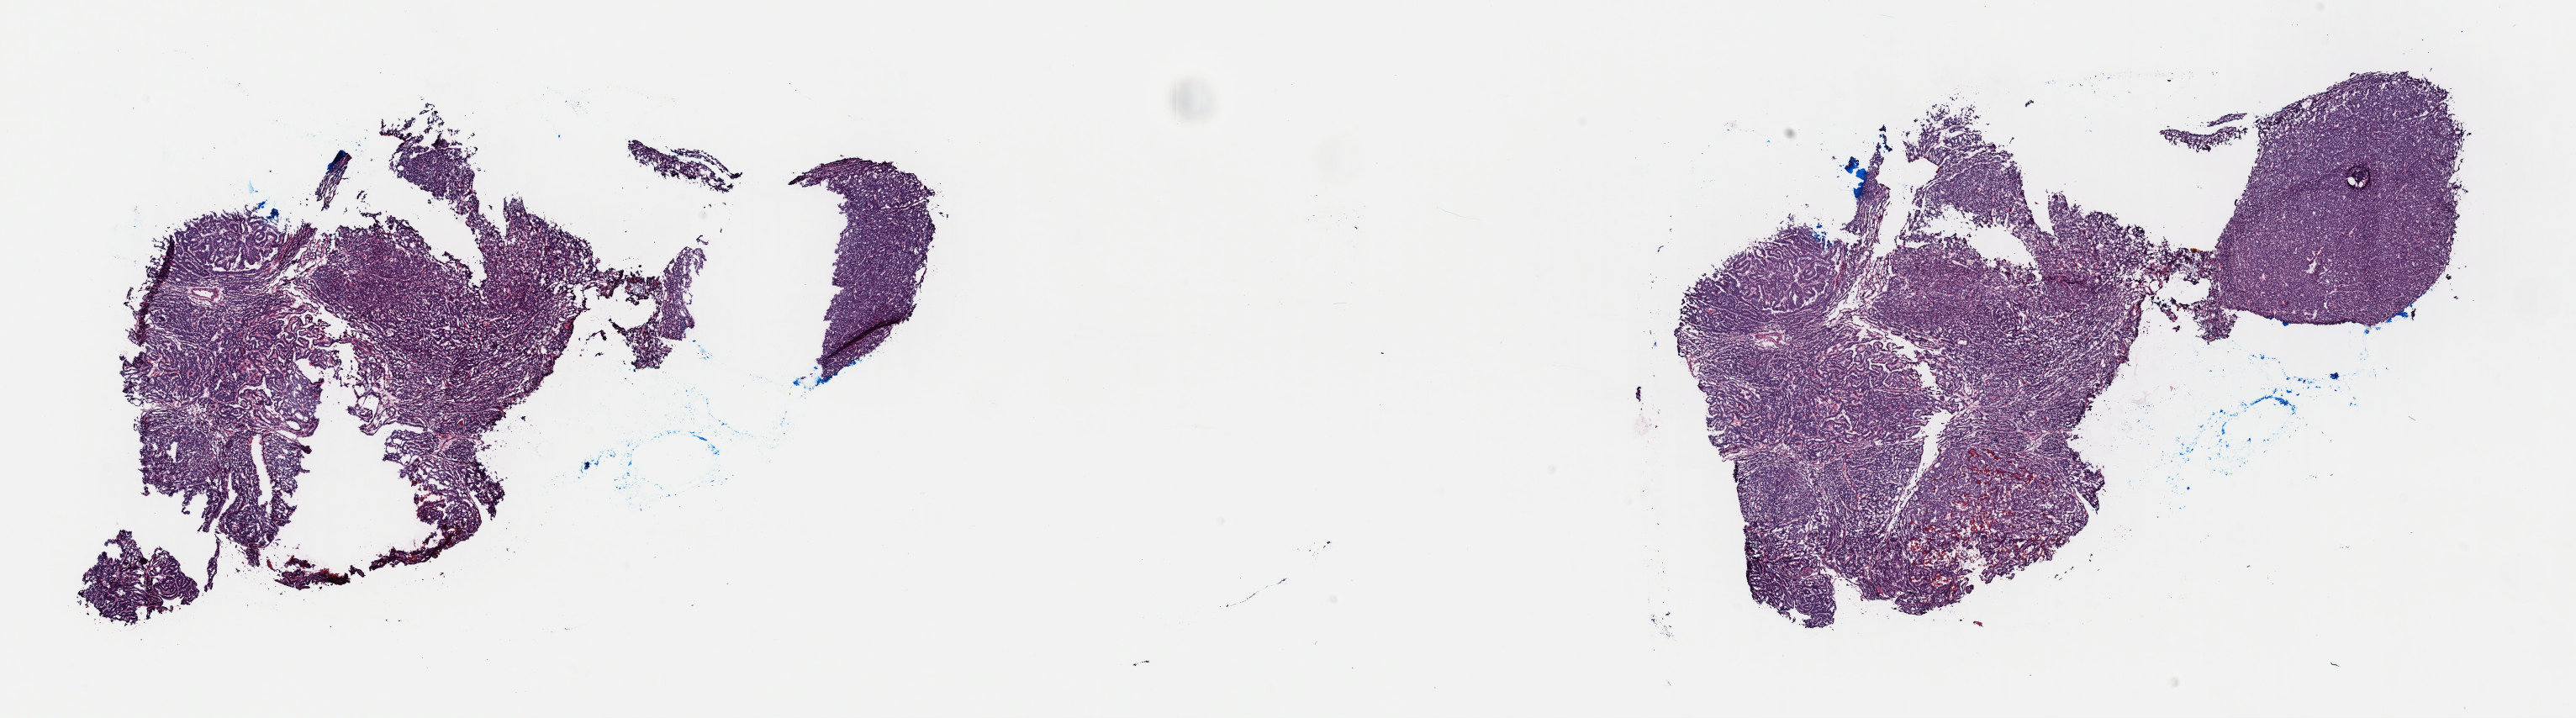
Digitized Hematoxylin and eosin (H&E) stained tissue section (whole slide), a low-resolution overview of the entire scanned area, about 24.2 x 6.7 mm (from a 40x scan), frozen section from the top of the tissue portion, sample: primary tumour, thyroid. Patient: female, age at initial diagnosis 51 years. Slide review estimates, as recorded: tumour cells 95%, tumour nuclei 95%, normal cells 0%, stromal cells 5%, necrosis 0%. Inflammatory infiltration, as recorded: lymphocyte infiltration 1%, monocyte infiltration 0%, neutrophil infiltration 0%.
- histologic diagnosis: Papillary adenocarcinoma, NOS (thyroid gland)
- laterality: bilateral
- AJCC pathologic stage: I